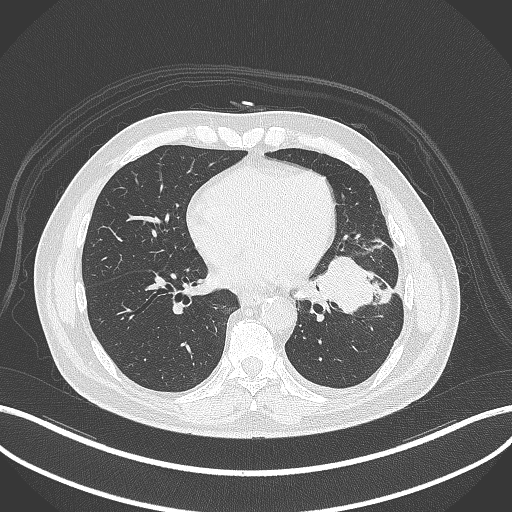
Chest CT, one axial slice. Slice 146 of 230 in the series (ordered by position). Lung window (W 1500 / L -600 HU). 1 mm slice thickness. 512 × 512 image matrix. Male patient, age 68 years. Case-level facts recorded for this patient, not image findings: clinical TNM (as recorded): T2b N0 M0.
Outlined on this slice (rectangle marked by the reading radiologist):
- lung tumour (recorded histology: squamous cell carcinoma): bounding box [x1, y1, x2, y2] px = [312, 254, 378, 319]